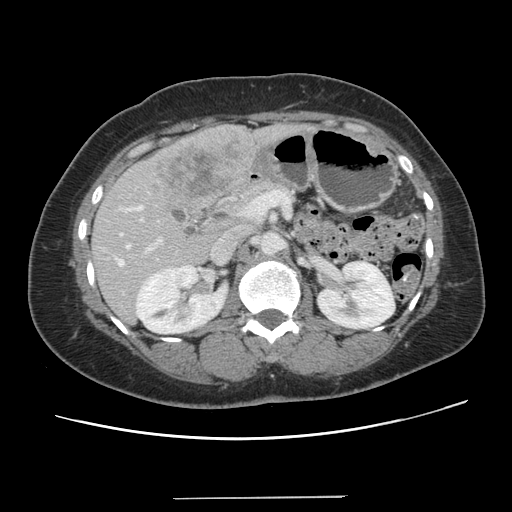
Contrast-enhanced abdominal CT, one axial slice. Position 63 of 141 along the scan axis. 120 kVp. Soft-tissue window (W 400 / L 40 HU). 2.5 mm slice thickness. 512 × 512 image matrix, field of view 366 × 366 mm. Female patient, age 53 years. Case-level facts recorded for this patient, not image findings: diagnosis: colorectal cancer liver metastases, imaged before liver resection; multiple liver metastases: no; largest metastasis: 14.5 cm; chemotherapy before resection: yes.
Annotated regions visible in this slice (manually delineated by an expert):
- hepatic veins: bounding box <116,244,129,265> (left, top, right, bottom; pixels)
- liver: <92,125,299,323>
- planned liver remnant (the part of the liver to remain after resection): <91,213,215,323>
- portal vein (with intrahepatic branches): <120,206,161,252>
- liver metastasis: <150,138,247,202>